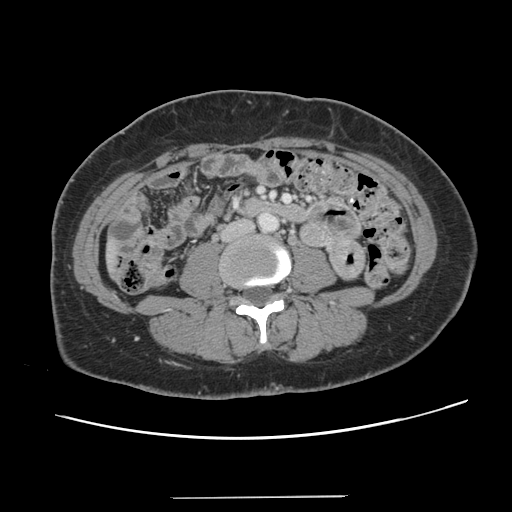
Contrast-enhanced abdominal CT, one axial slice. 120 kVp. Intravenous contrast given. Soft-tissue window (W 400 / L 40 HU). 512 × 512 image matrix, field of view 366 × 366 mm. Female patient, age 53 years. Case-level facts recorded for this patient, not image findings: diagnosis: colorectal cancer liver metastases, imaged before liver resection; multiple liver metastases: no; largest metastasis: 14.5 cm; chemotherapy before resection: yes.
Outlined on this slice (outlined manually by an expert reader):
- liver: bounding box [x1, y1, x2, y2] px = [109, 242, 118, 266]
- planned liver remnant (the part of the liver to remain after resection): [109, 244, 115, 267]